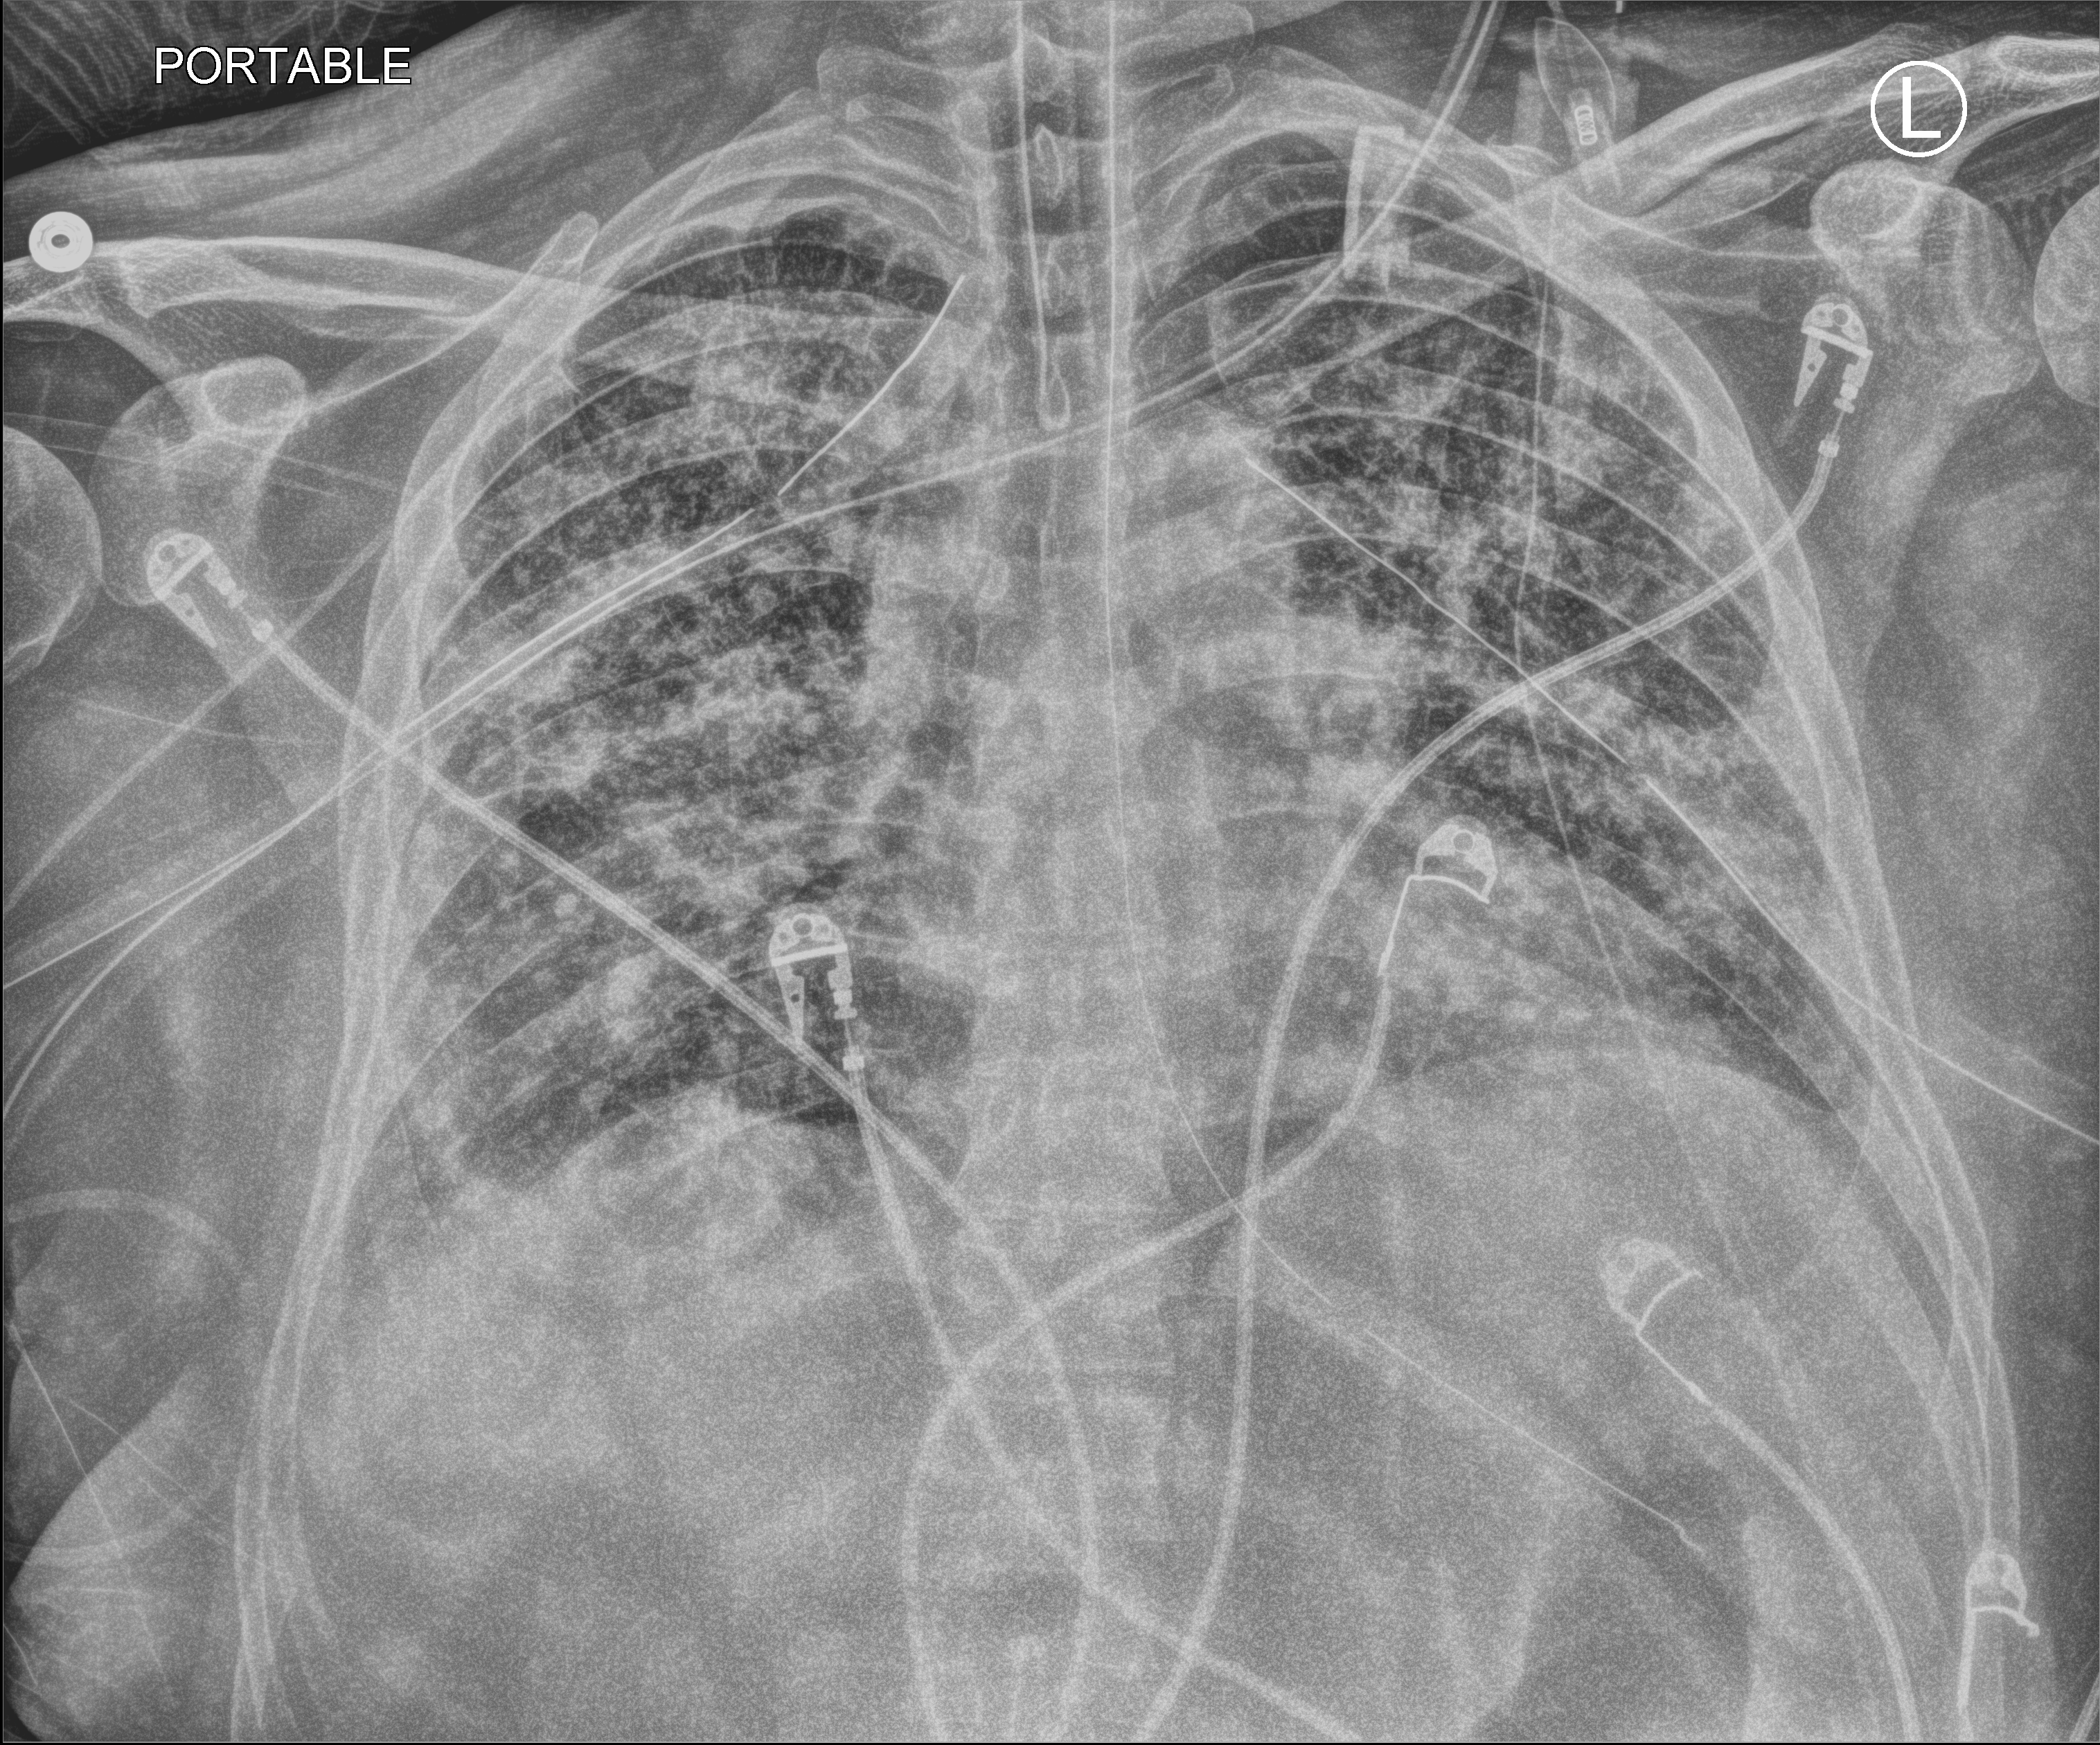
Chest X-ray (portable); anteroposterior (AP) projection. Patient hospitalised with COVID-19; male, aged 18–59 years.
Hospital-stay facts (about this admission, not read from this image; timing relative to this image not recorded): admitted to intensive care during this hospital stay: yes.